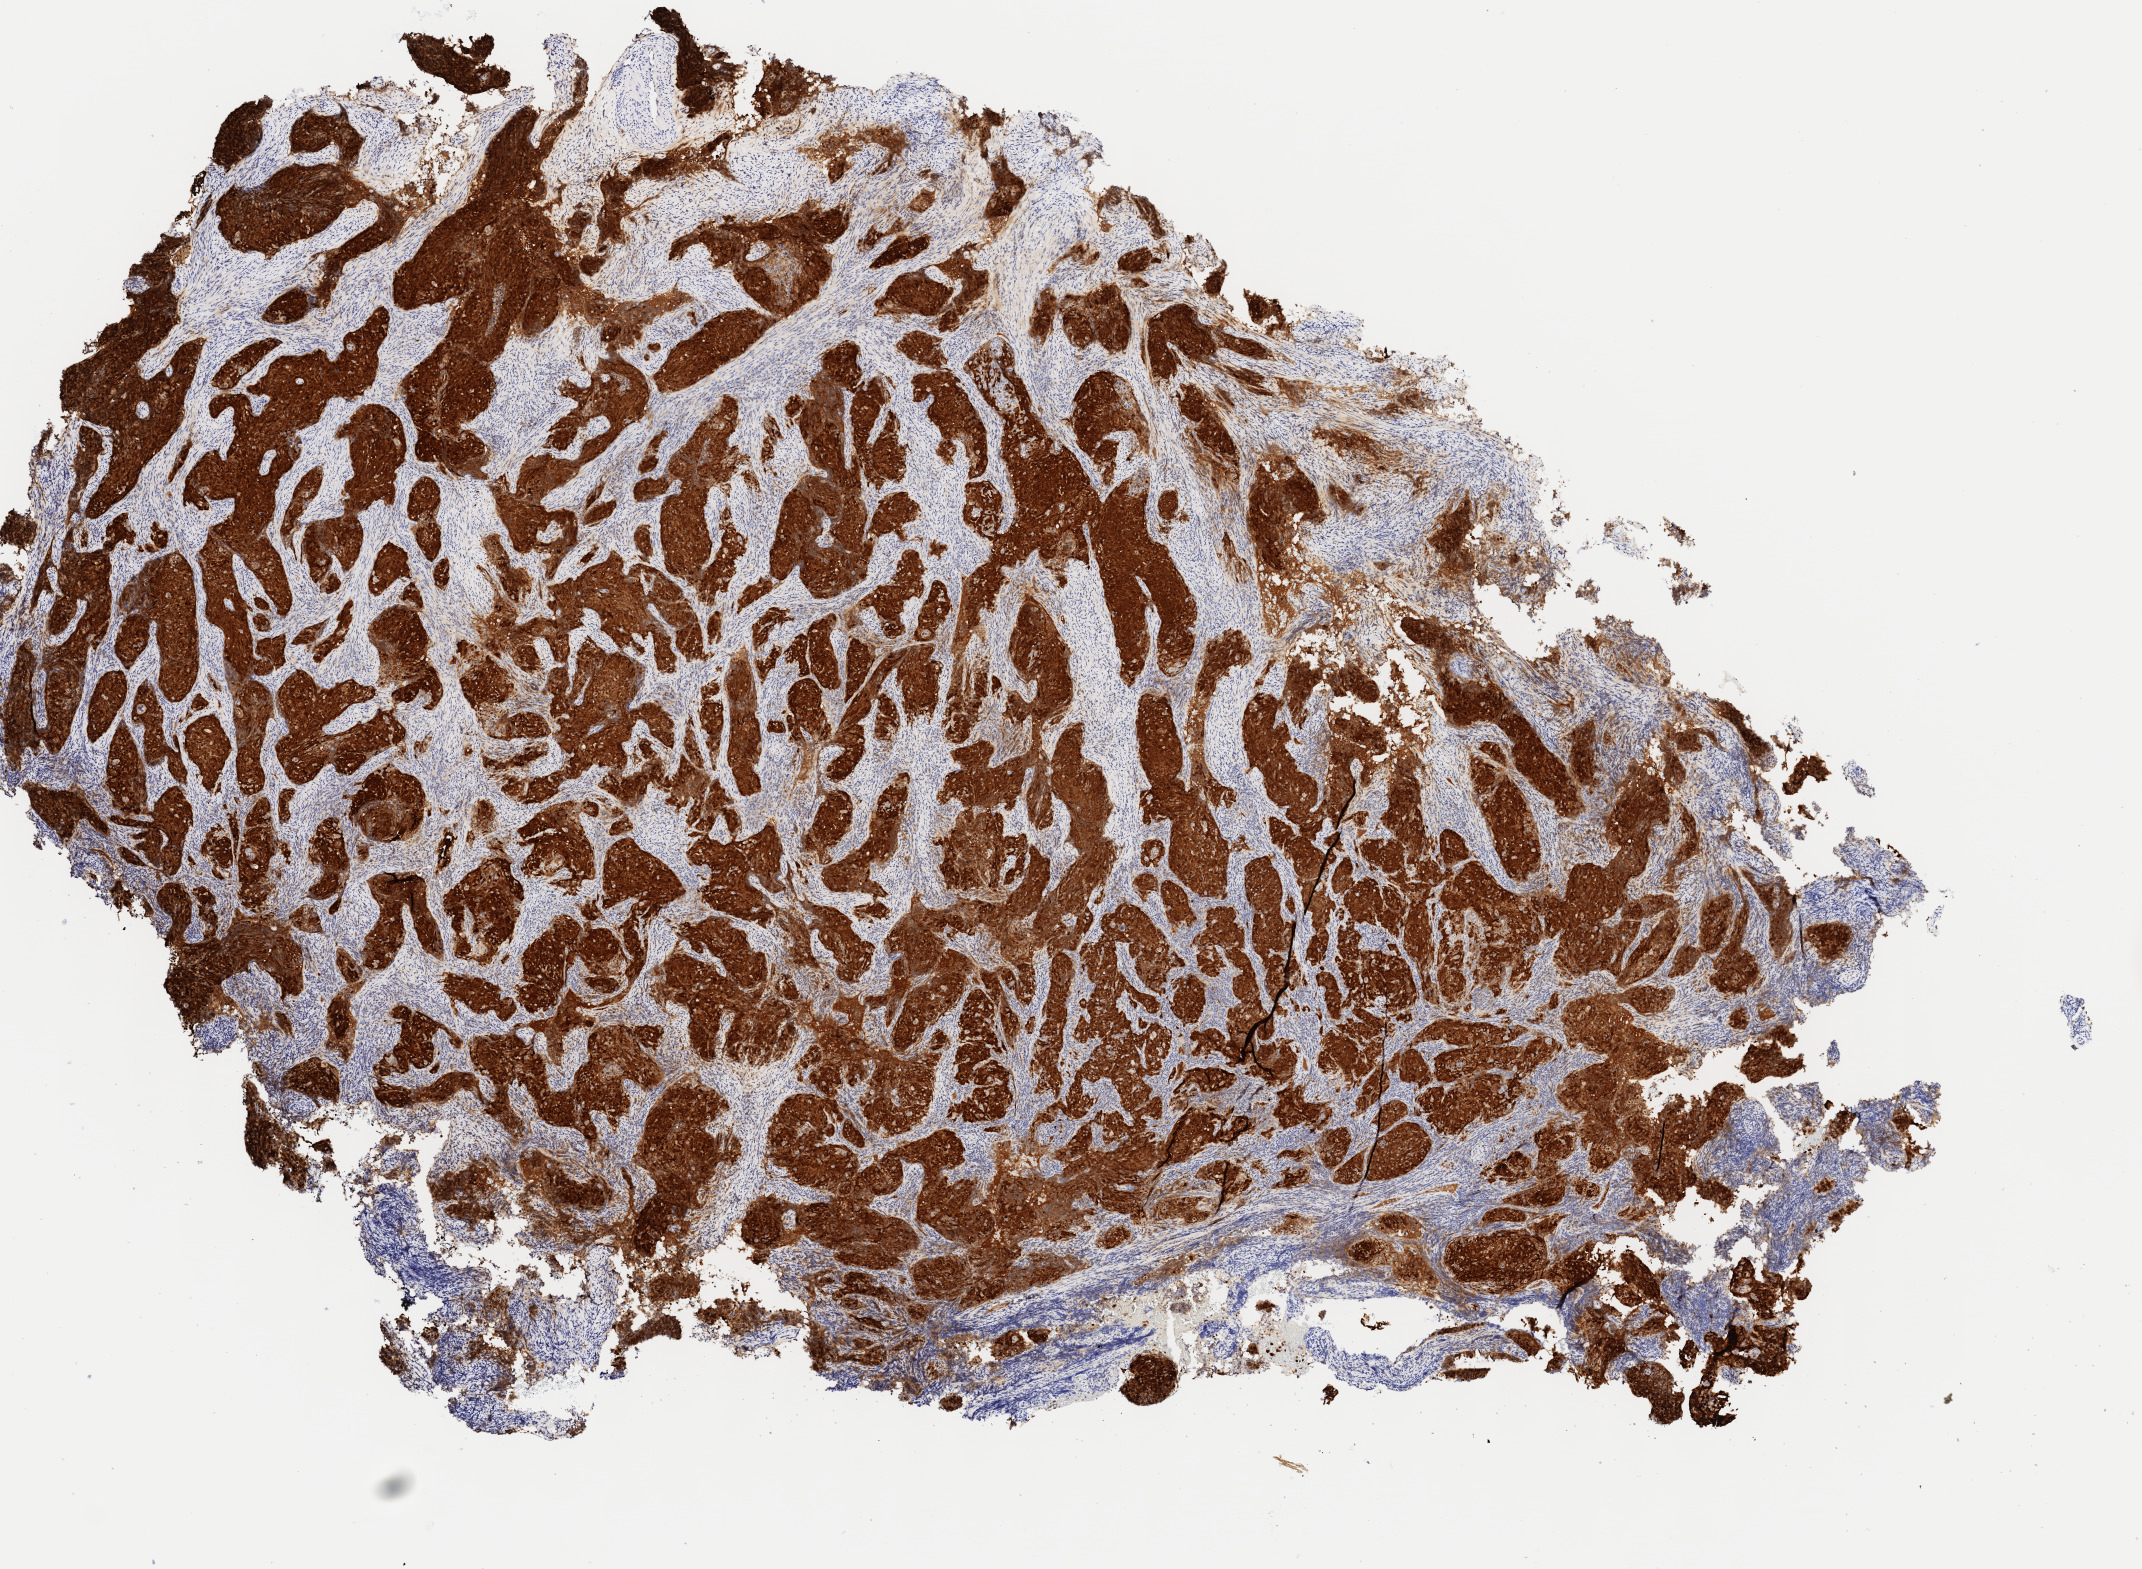
Immunohistochemistry (IHC) whole-slide image stained for p16 (p16INK4a), shown as a low-resolution overview of the whole scanned area (about 8.5 x 6.2 mm). Tumor tissue. Site: cervix. Female patient, 51 years old.
Diagnosis: Squamous cell carcinoma, large cell, nonkeratinizing, NOS.